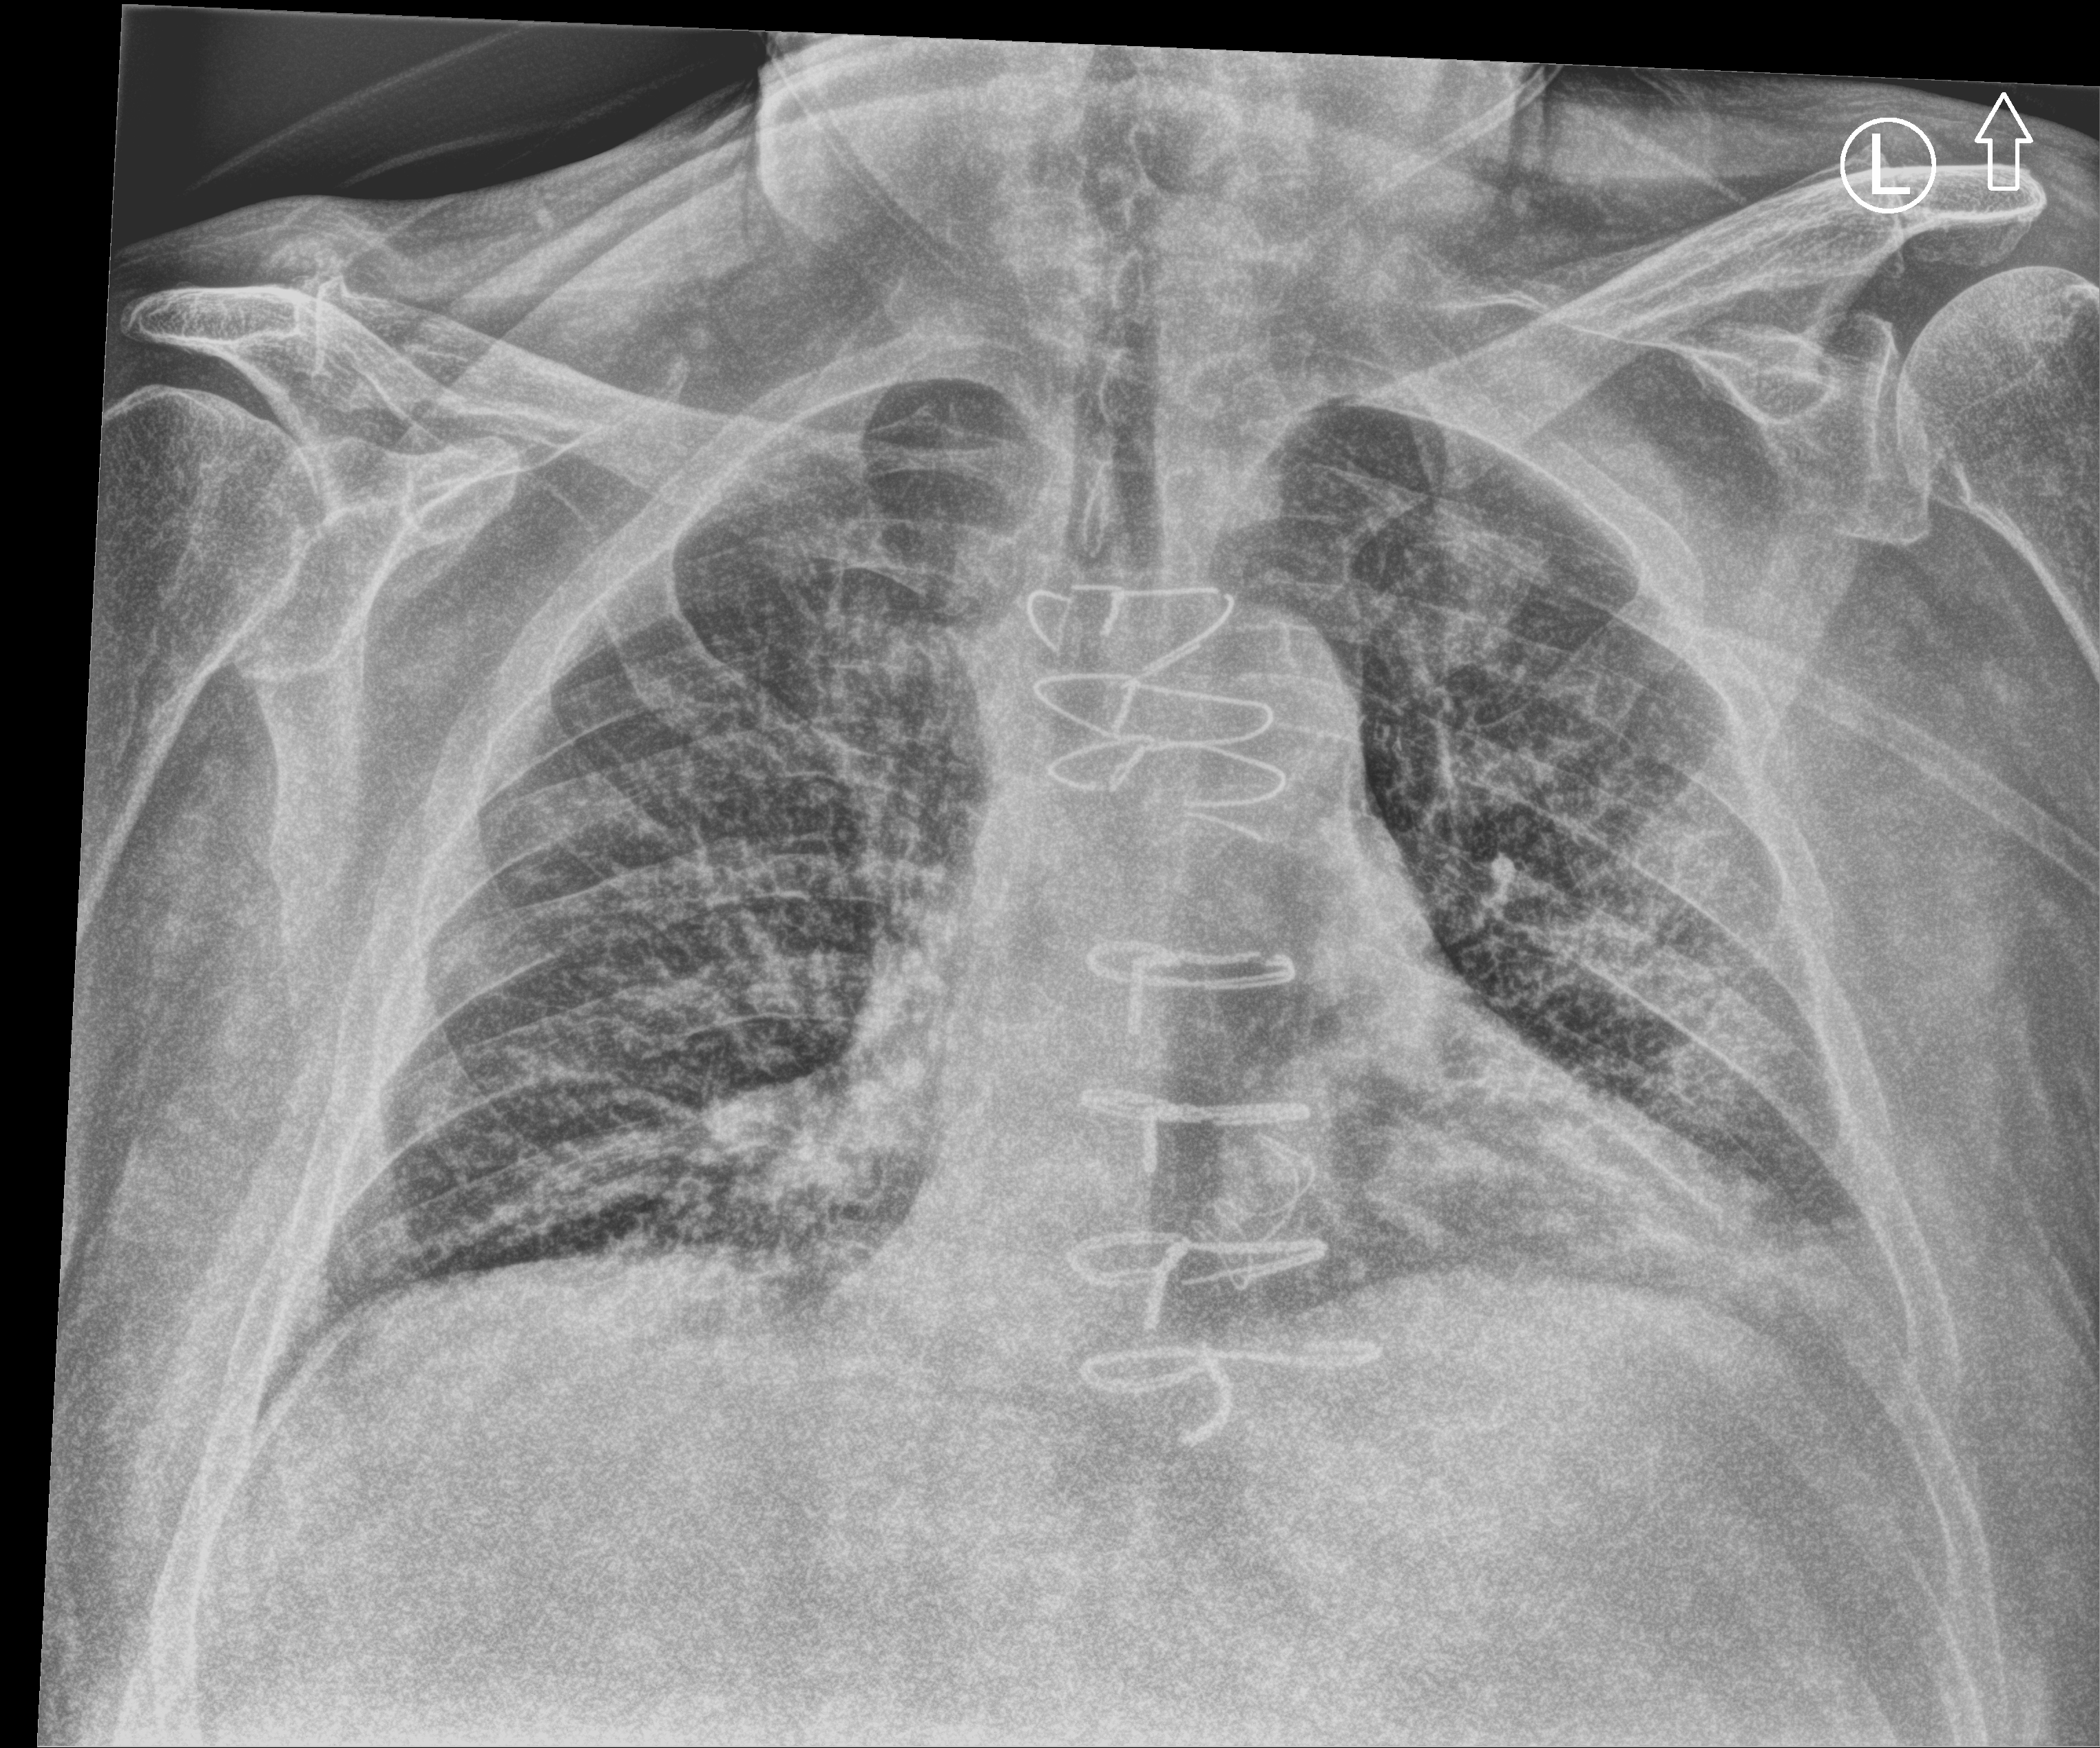
Bedside chest radiograph (computed radiography); anteroposterior (AP) projection. Patient hospitalised with COVID-19; male, aged 75–90 years.
Hospital-stay facts (about this admission, not read from this image; timing relative to this image not recorded):
- mechanically ventilated during this hospital stay: no
- admitted to intensive care during this hospital stay: no